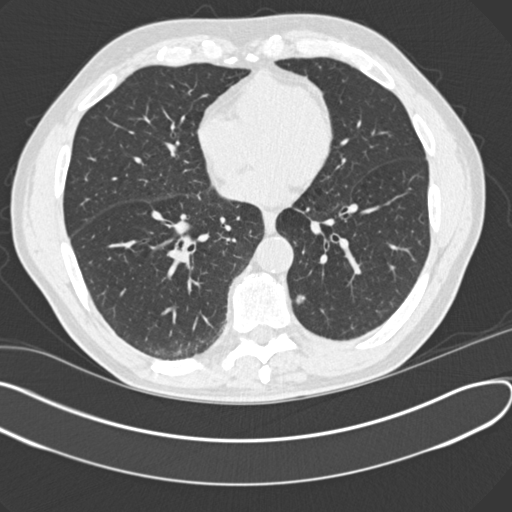
Low-dose screening chest CT, one axial slice; slice 68 of 166 in the series (ordered by position); reconstruction kernel B30f; 120 kVp; lung window (W 1500 / L -600 HU); 2 mm slice thickness; 512 × 512 image matrix, field of view 372 × 372 mm.
Structures marked on this image (manually delineated by an expert):
- lesion 1 (tumor, lower lobe of left lung): bounding box (x1, y1, x2, y2) in pixels: (294, 293, 306, 304)